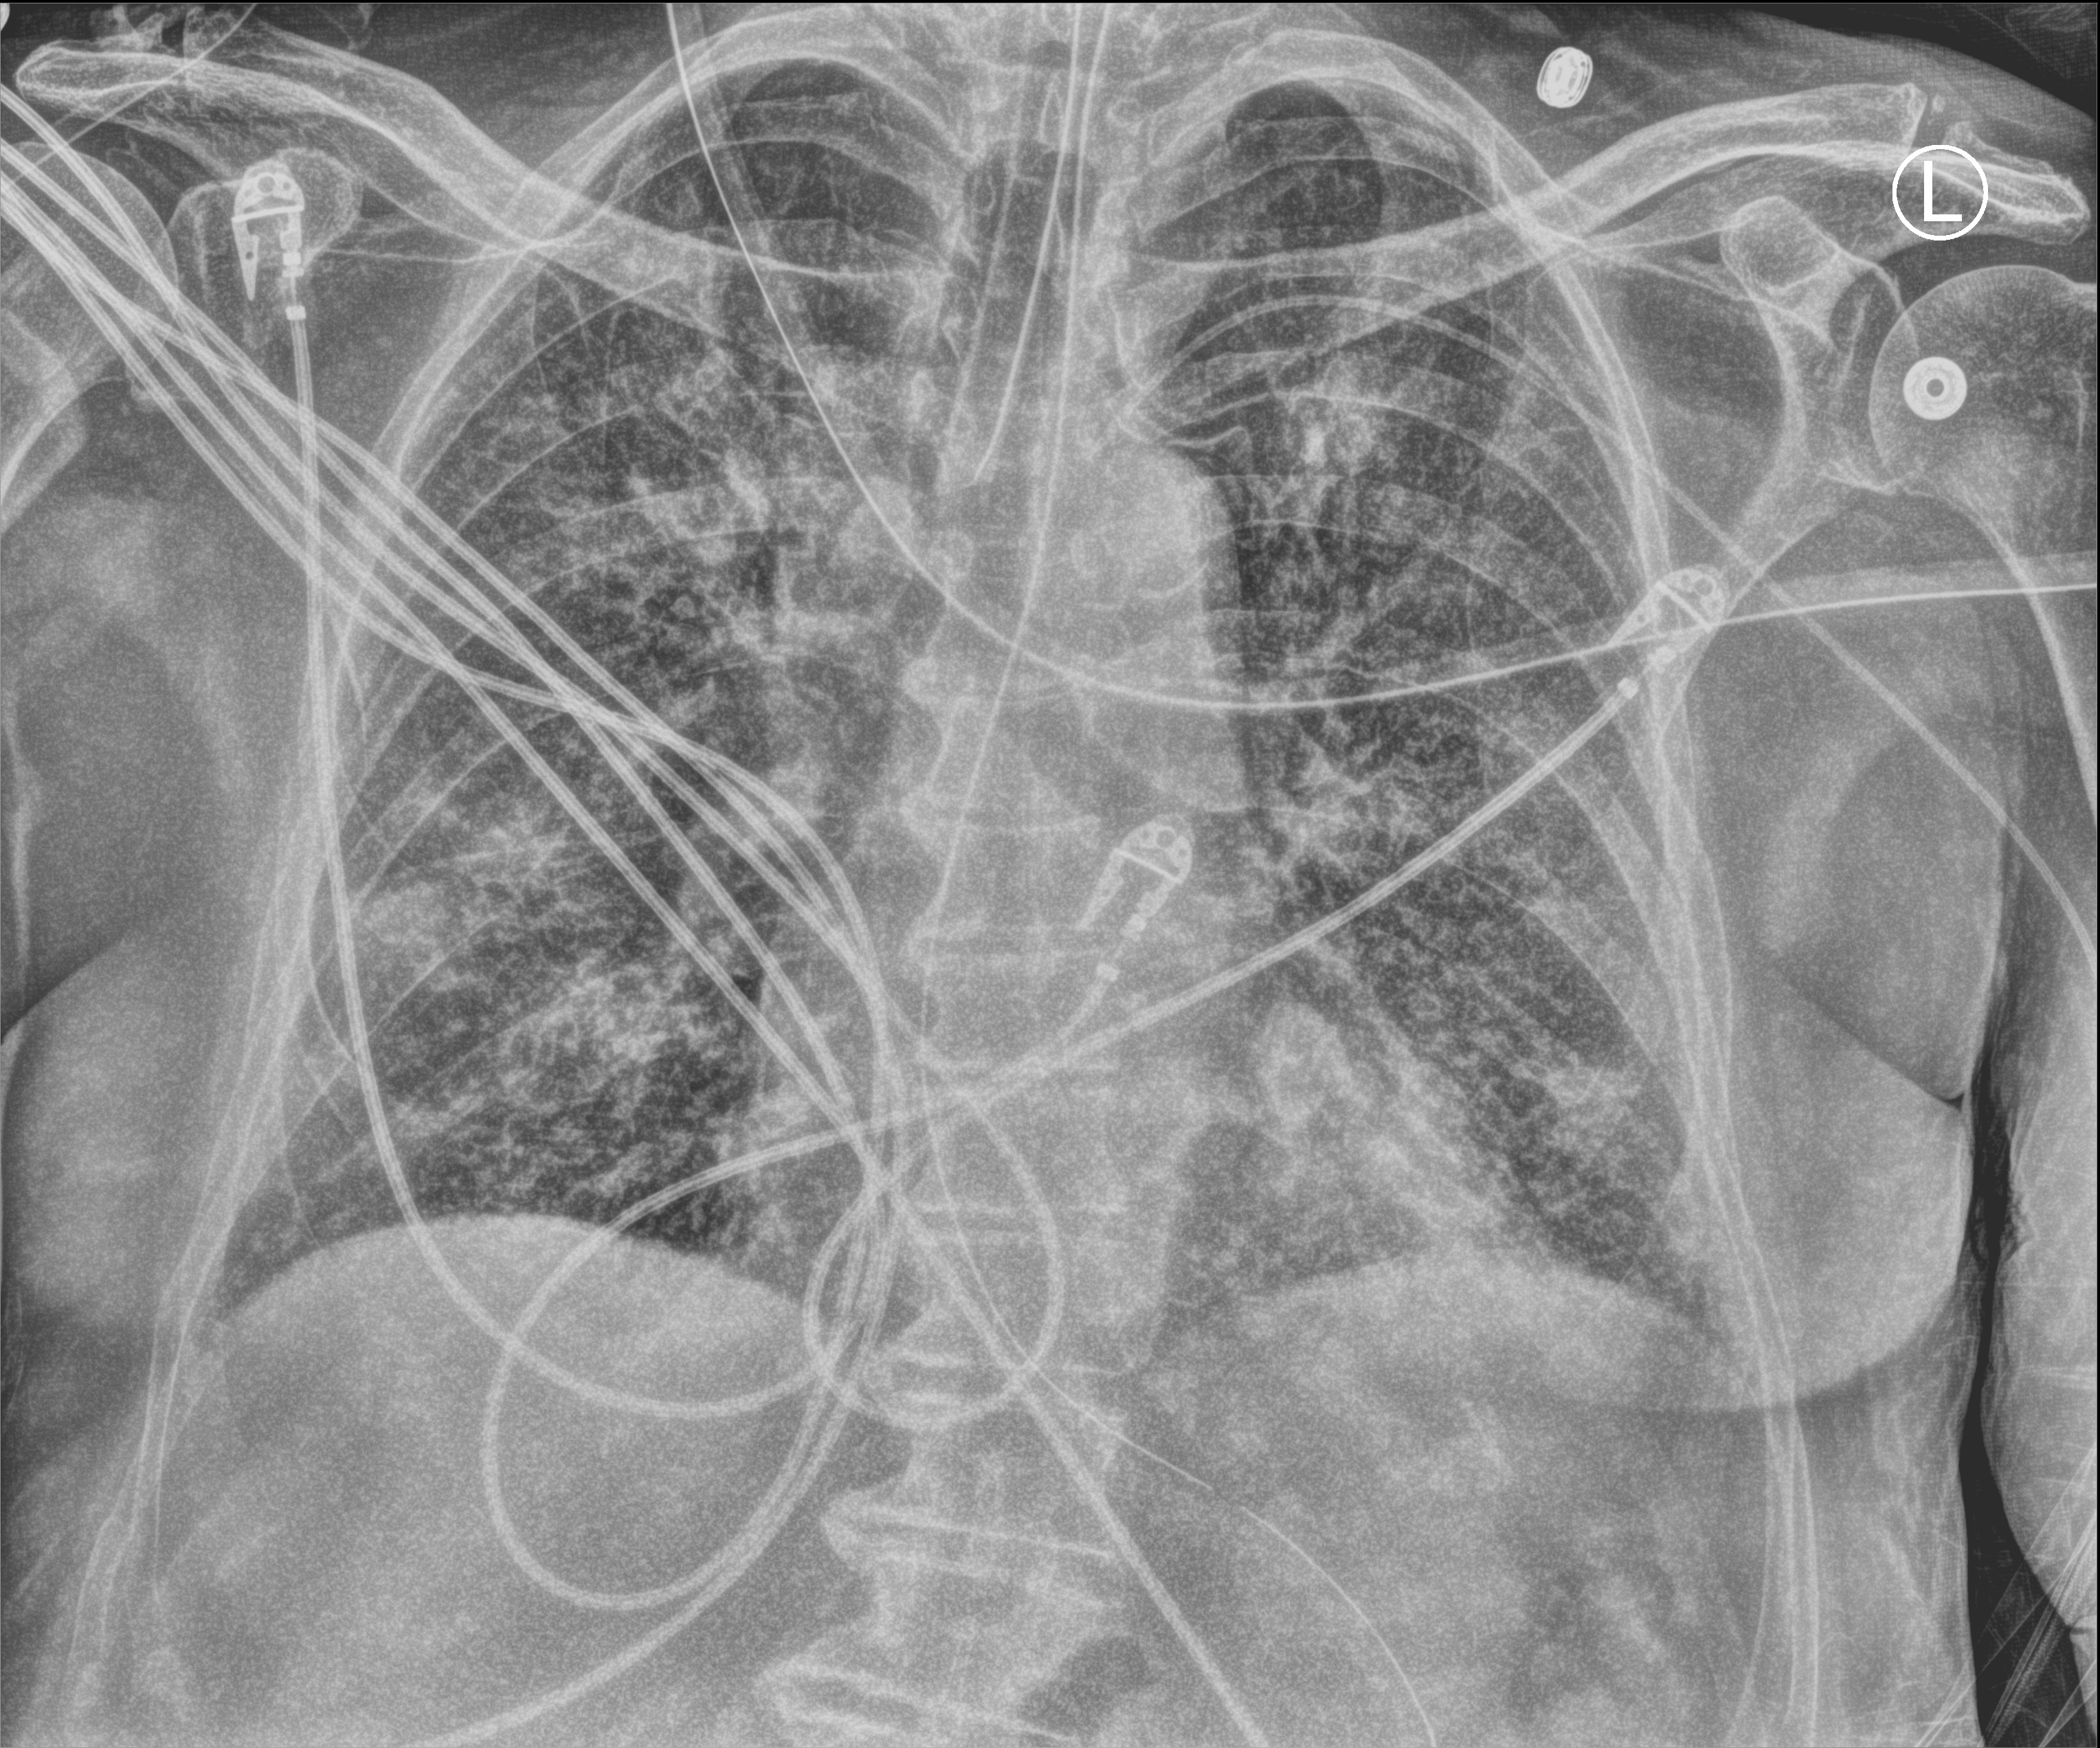
Chest X-ray (portable); anteroposterior (AP) projection. Male patient hospitalised with COVID-19, age 75–90 years.
Admission-level facts for this patient (not findings on this image; timing relative to this image not recorded): other chronic lung disease (admission record): no.